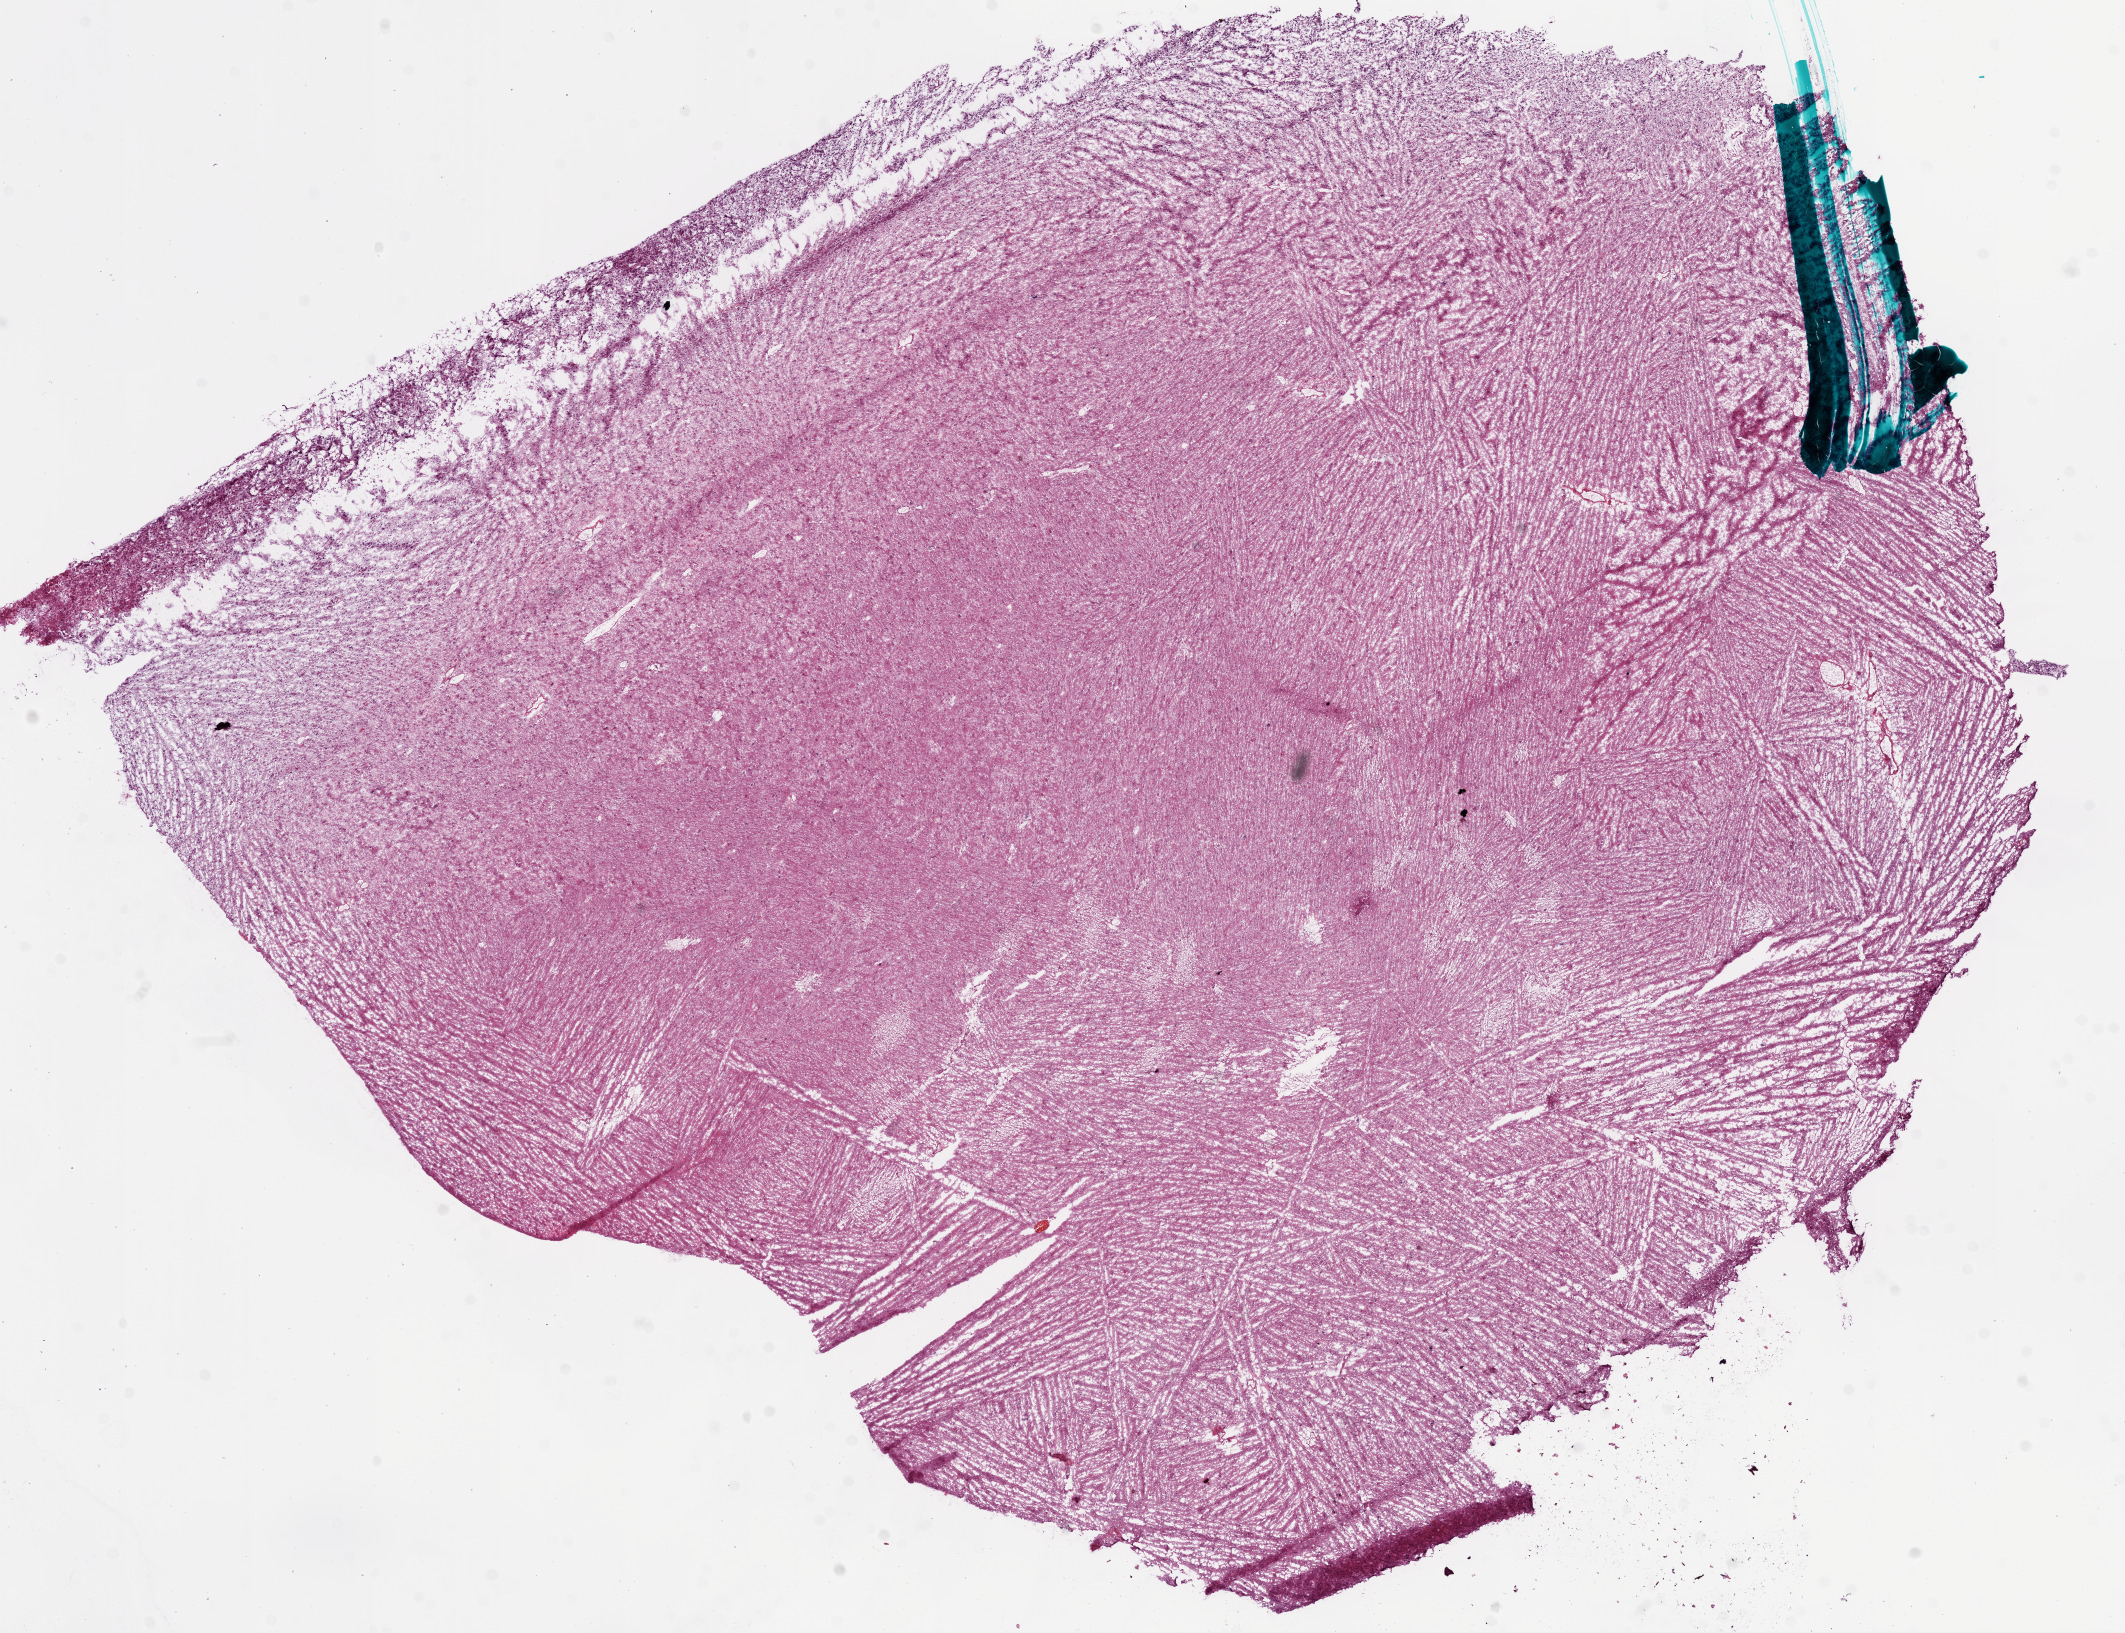
Digitized H&E tissue section (whole slide) — shown as a low-resolution overview of the whole scanned area (about 17.1 x 13.1 mm). Frozen section. Sample: primary tumour, brain. Male patient; age at initial diagnosis 21 years. Composition of this section per pathologist review: tumour cells 20%, tumour nuclei 40%.
Histologic diagnosis: Glioblastoma.